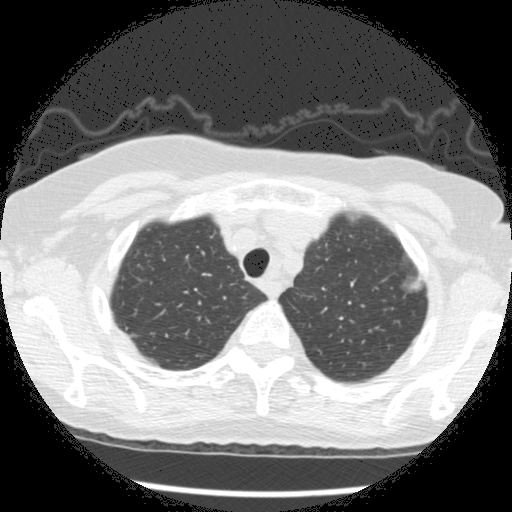
Low-dose screening chest CT, axial slice; second annual screen; lung window (W 1500 / L -600 HU); 120 kVp; slice 34 of 266 in the series. Female, age 73 years at enrolment.
Expert-annotated lung lesion, bounding box (x1, y1, x2, y2) in pixels: (385, 252, 430, 298). The screening reader recorded 3 non-calcified nodules or masses ≥4 mm on this exam; which of them this box marks is not recorded. Lung cancer was diagnosed 49 days after this screen: bronchiolo-alveolar adenocarcinoma, NOS, left upper lobe, well differentiated (G1), stage IA (AJCC 6th edition), 10 mm at pathology.